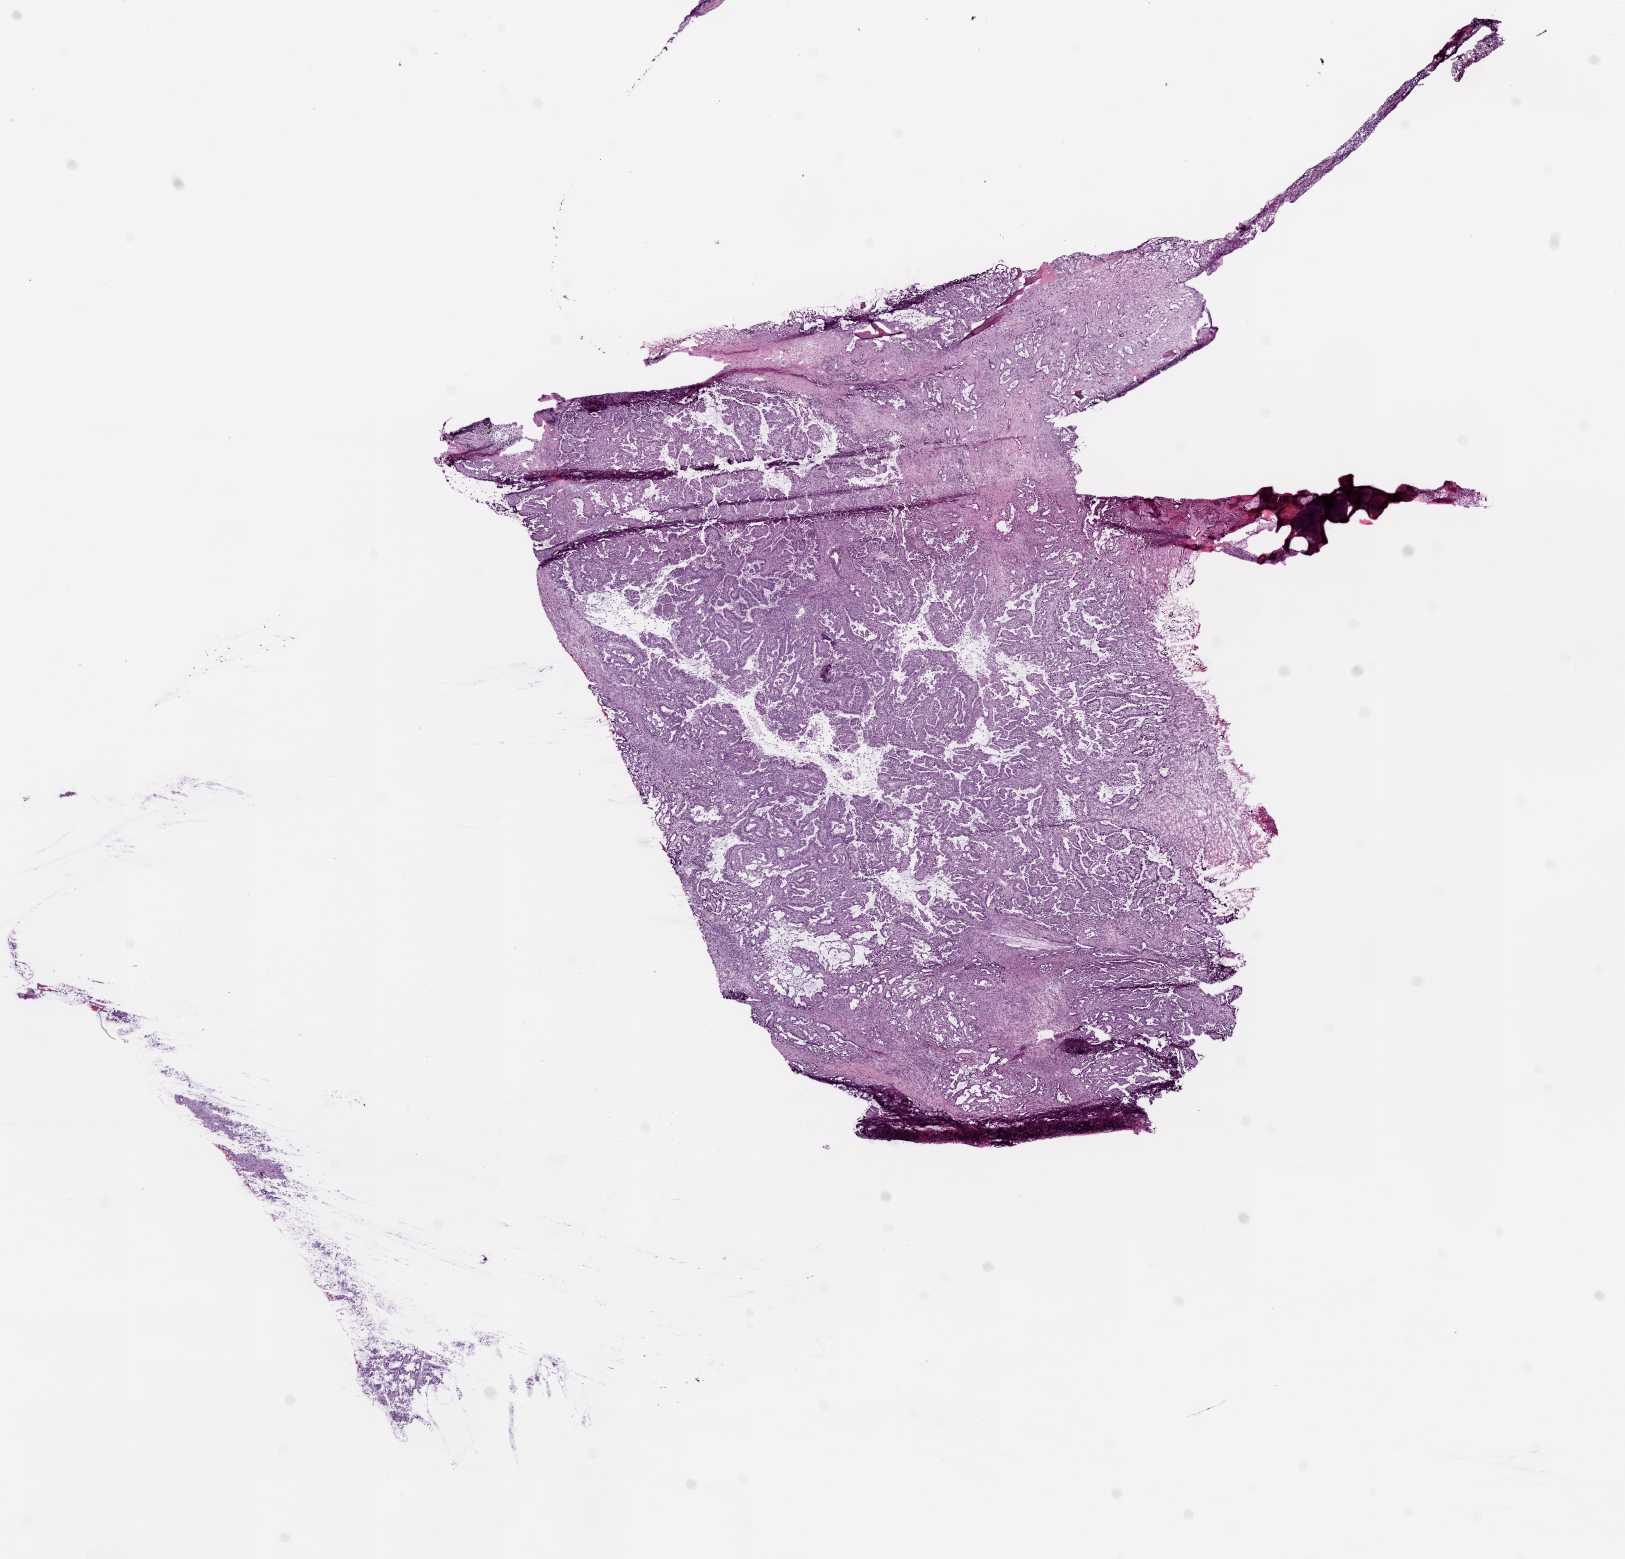
Digitized Hematoxylin and eosin (H&E) stained tissue section (whole slide), low-resolution overview of the scanned area, about 13.0 x 12.5 mm, frozen section from the top of the tissue portion, primary tumour sample from the lung. Patient: female, age at initial diagnosis 70 years. Composition of this section per pathologist review: tumour cells 75%, tumour nuclei 80%, normal cells 0%, stromal cells 25%, necrosis 0%. Inflammatory infiltration, as recorded: lymphocyte infiltration 10%.
Histologic diagnosis: Adenocarcinoma with mixed subtypes (middle lobe, lung). AJCC pathologic stage: IV (6th edition).